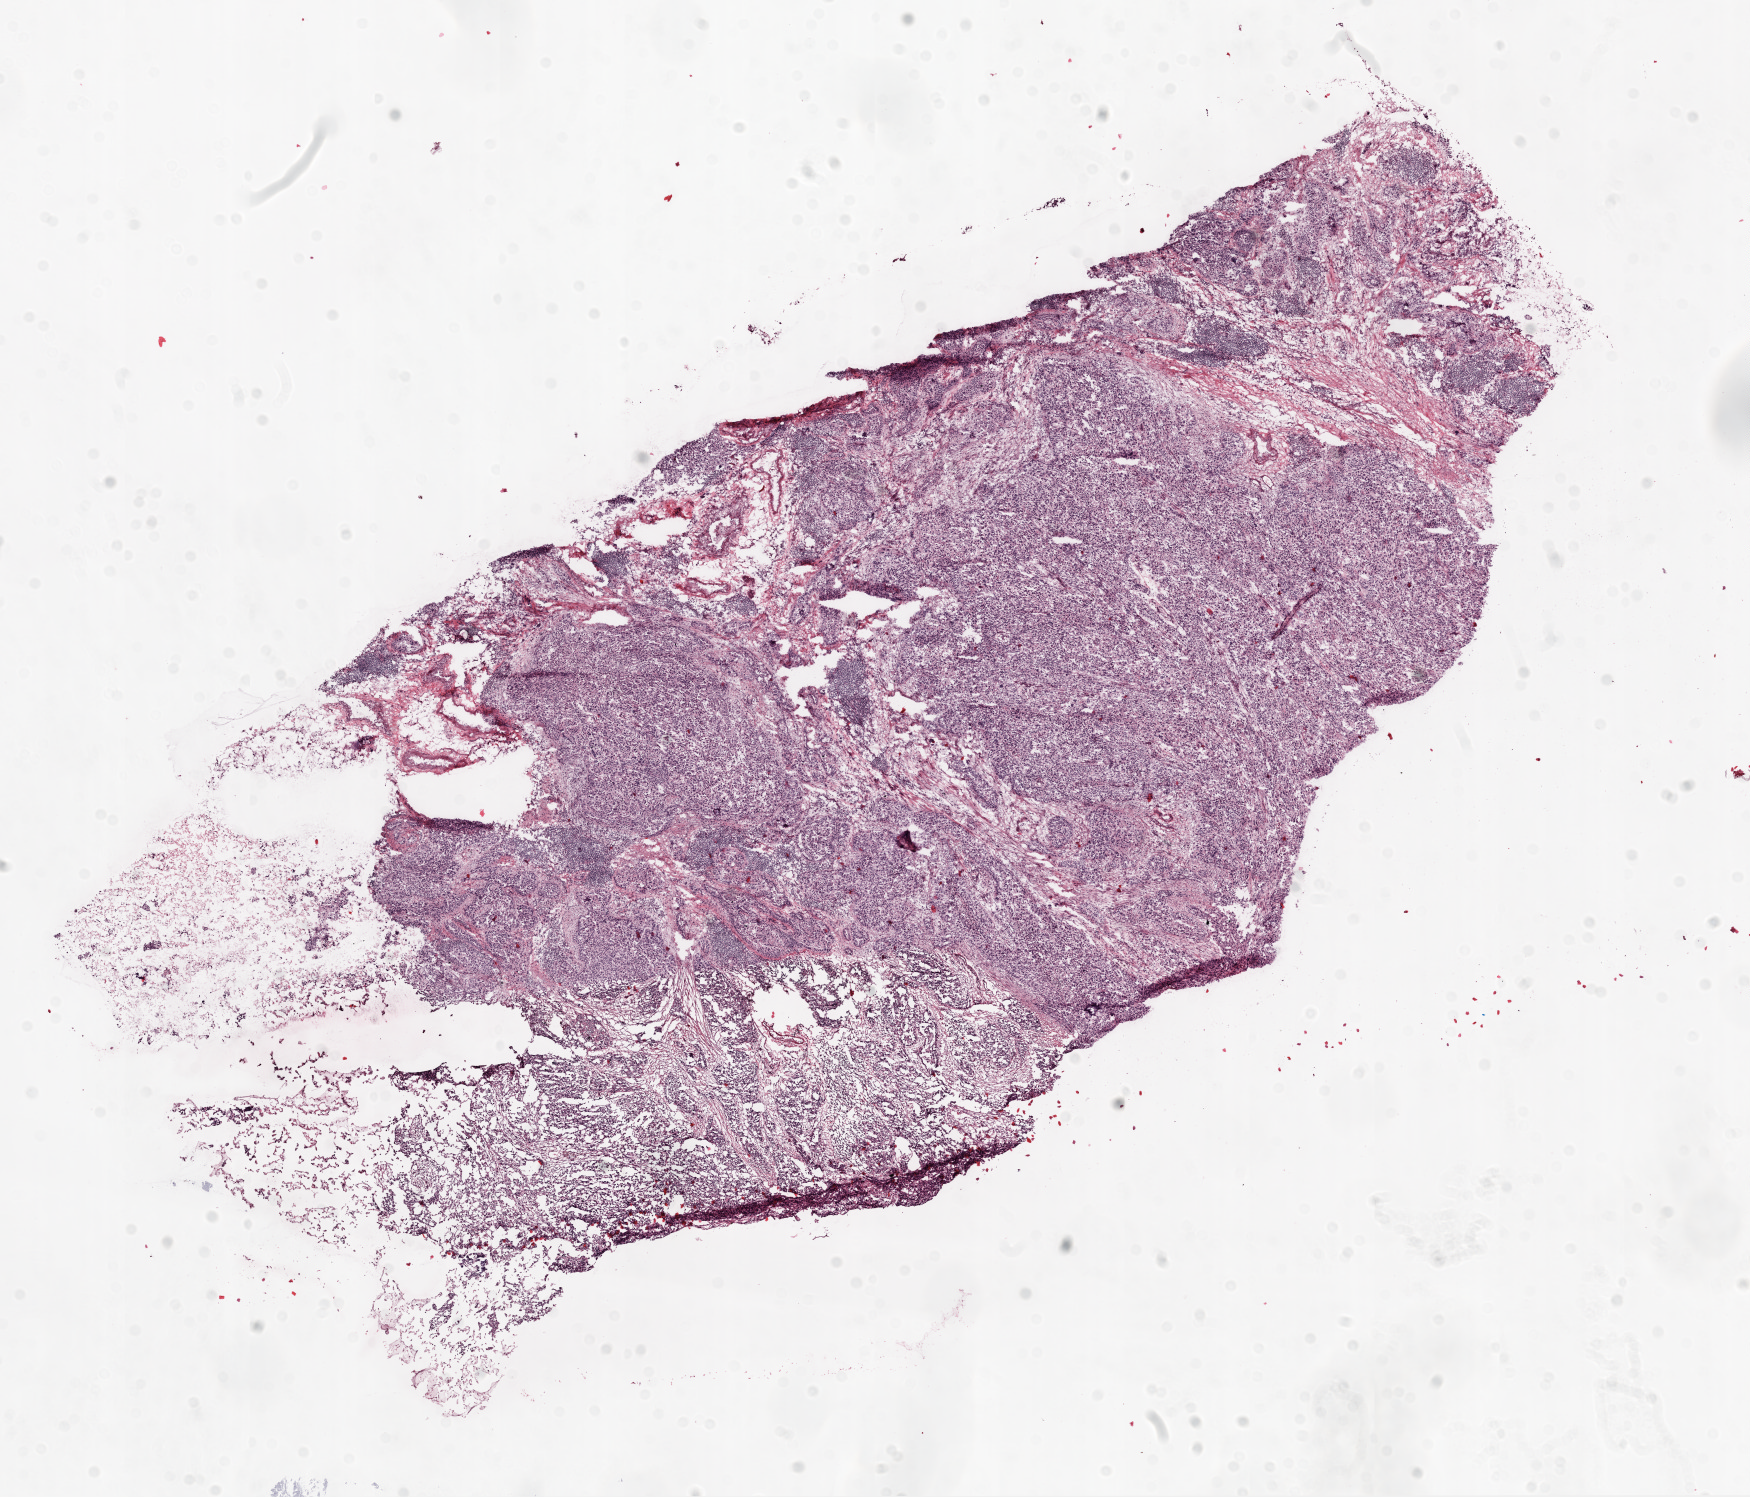
Whole-slide histology image, H&E, whole scanned area (about 14.0 x 12.0 mm) shown as a low-resolution overview, frozen section from the top of the tissue portion, primary tumour sample from the ovary. Patient: female, age at initial diagnosis 61 years. Histologic grade: G3 (poorly differentiated). Slide review estimates, as recorded: tumour cells 90%, tumour nuclei 95%, normal cells 0%, stromal cells 10%, necrosis 0%.
Laterality: bilateral. Diagnosis: Serous cystadenocarcinoma, NOS. FIGO stage: IIIC.